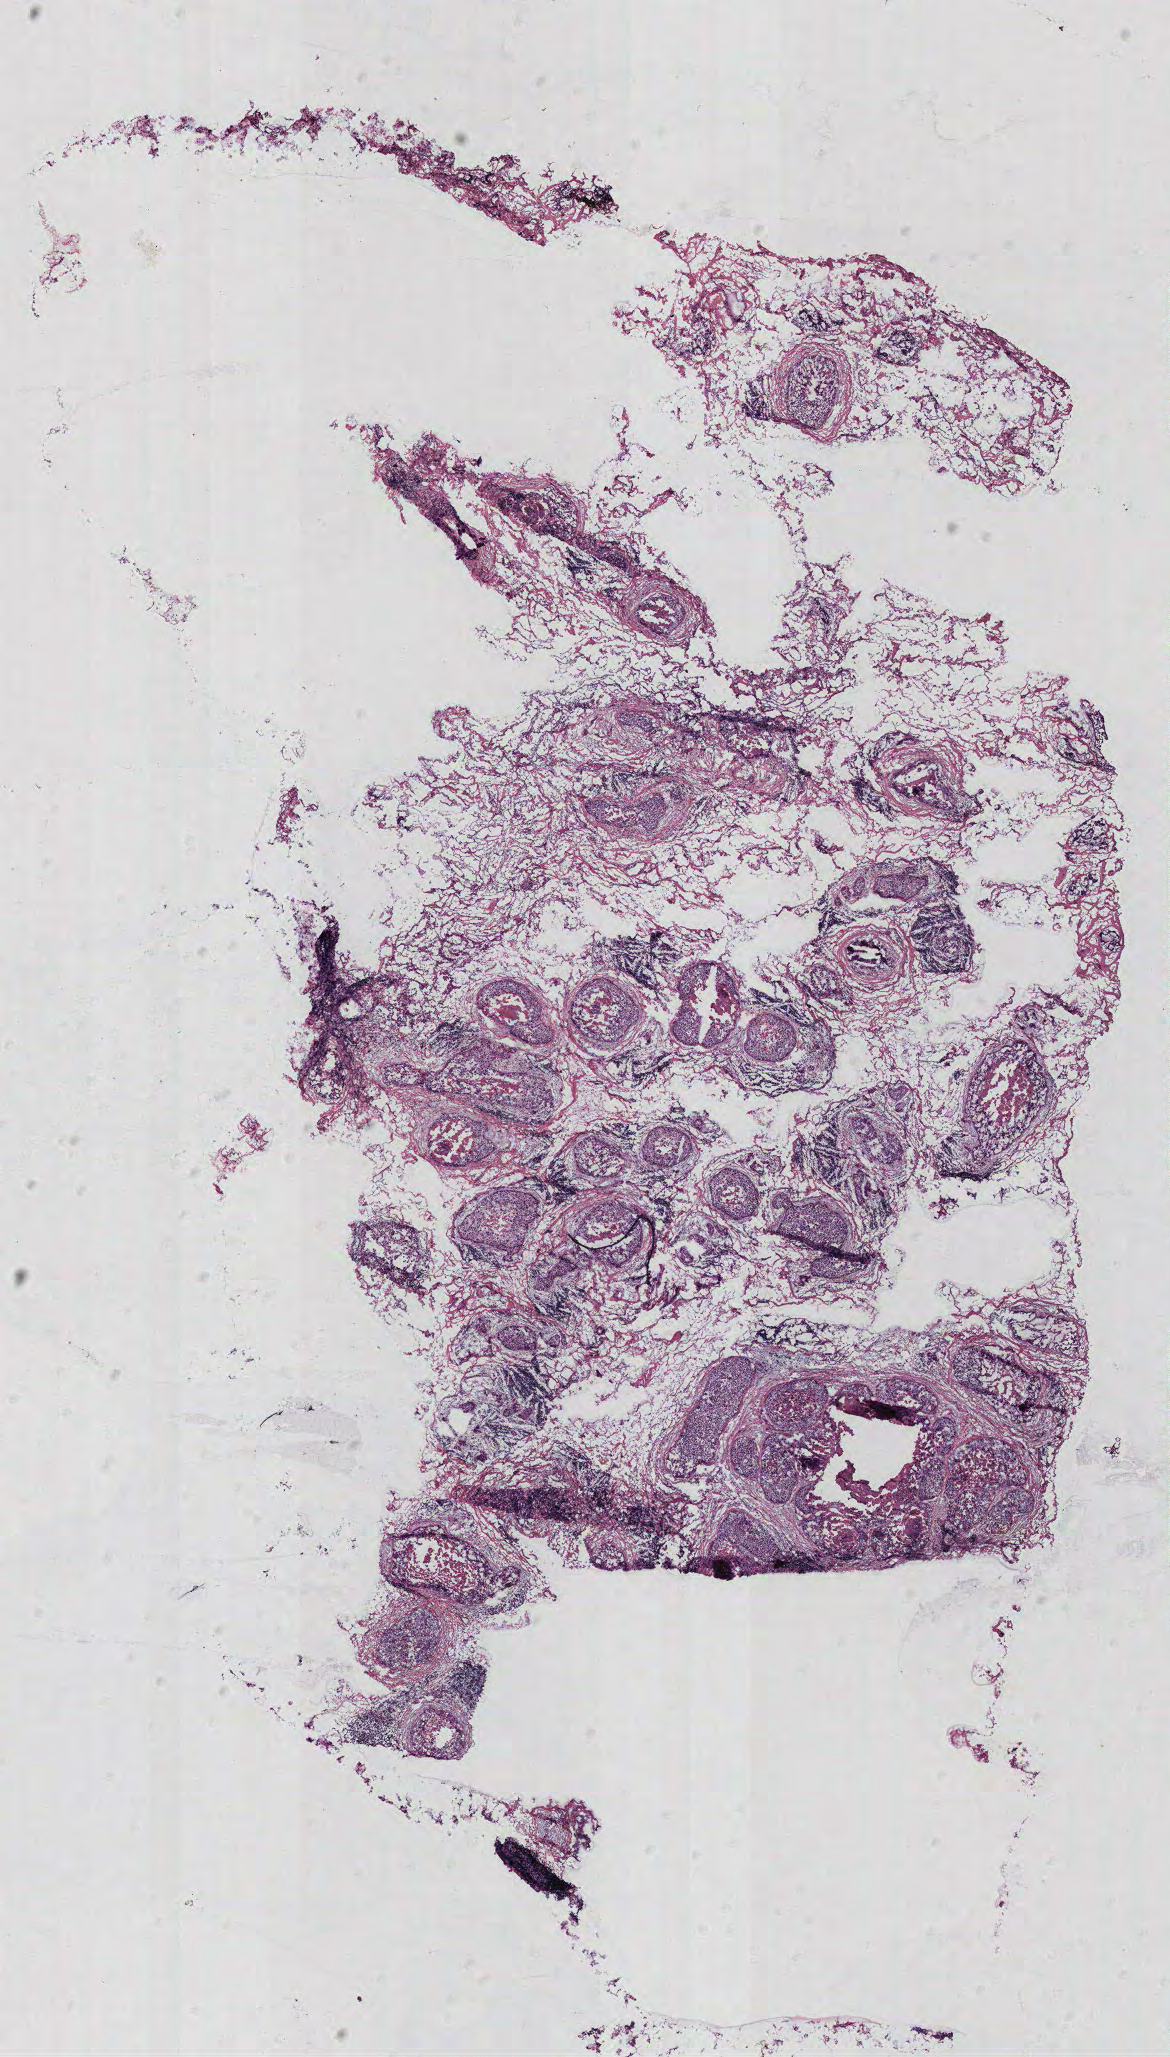
Hematoxylin and eosin (H&E) stained whole-slide image — low-resolution overview of the scanned area, about 9.4 x 16.5 mm; breast, tissue type not recorded. Female, 63 y/o.
* patient diagnosis: Infiltrating duct carcinoma, NOS